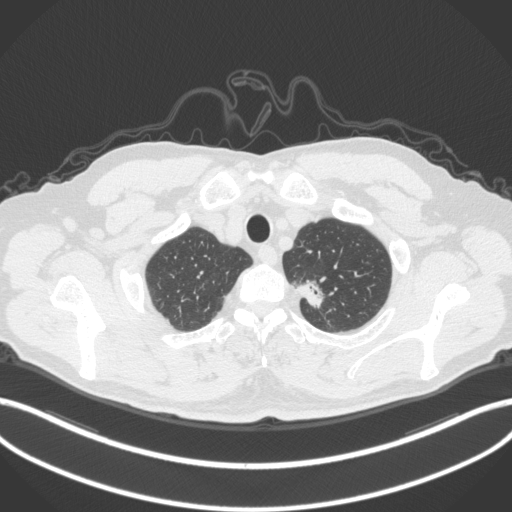
Chest CT, one axial slice. Slice 339 of 382 in the series (ordered by position). Reconstruction kernel B31f. 120 kVp. Lung window (W 1500 / L -600 HU). 1 mm slice thickness. 512 × 512 image matrix, field of view 400 × 400 mm. Male patient, age 64 years. From the clinical record (not read from this slice): clinical TNM (as recorded): T1c N0 M0.
Annotated regions visible in this slice (bounding box drawn by a radiologist):
- lung tumour (recorded histology: adenocarcinoma): bounding box (x1, y1, x2, y2) in pixels: (291, 271, 333, 314)